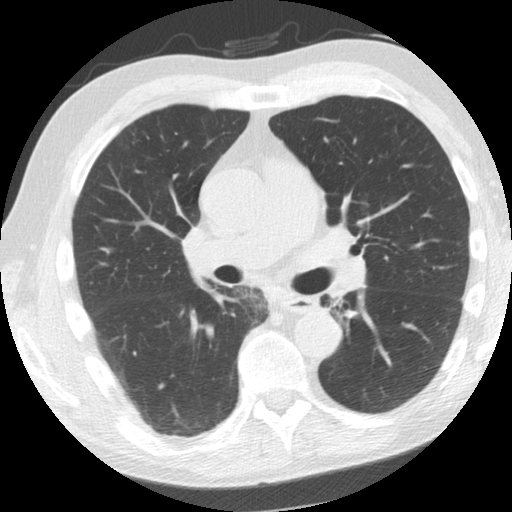
Low-dose screening chest CT, axial slice, second annual screen, lung window (W 1500 / L -600 HU), 2.5 mm slice thickness, standard (soft-tissue) reconstruction kernel (STANDARD), 512 × 512 image matrix, field of view 324 × 324 mm. Male participant, aged 61 years at enrolment. Former smoker at enrolment.
Expert-annotated lung lesion, bounding box [x1, y1, x2, y2] px = [304, 287, 348, 323]. No non-calcified nodule or mass ≥4 mm was recorded by the screening reader at this exam. Later outcome: lung cancer diagnosed 775 days after this screen — squamous cell carcinoma, NOS, left upper lobe, left lower lobe, well differentiated (G1), stage IIB (AJCC 6th edition), 100 mm at pathology.